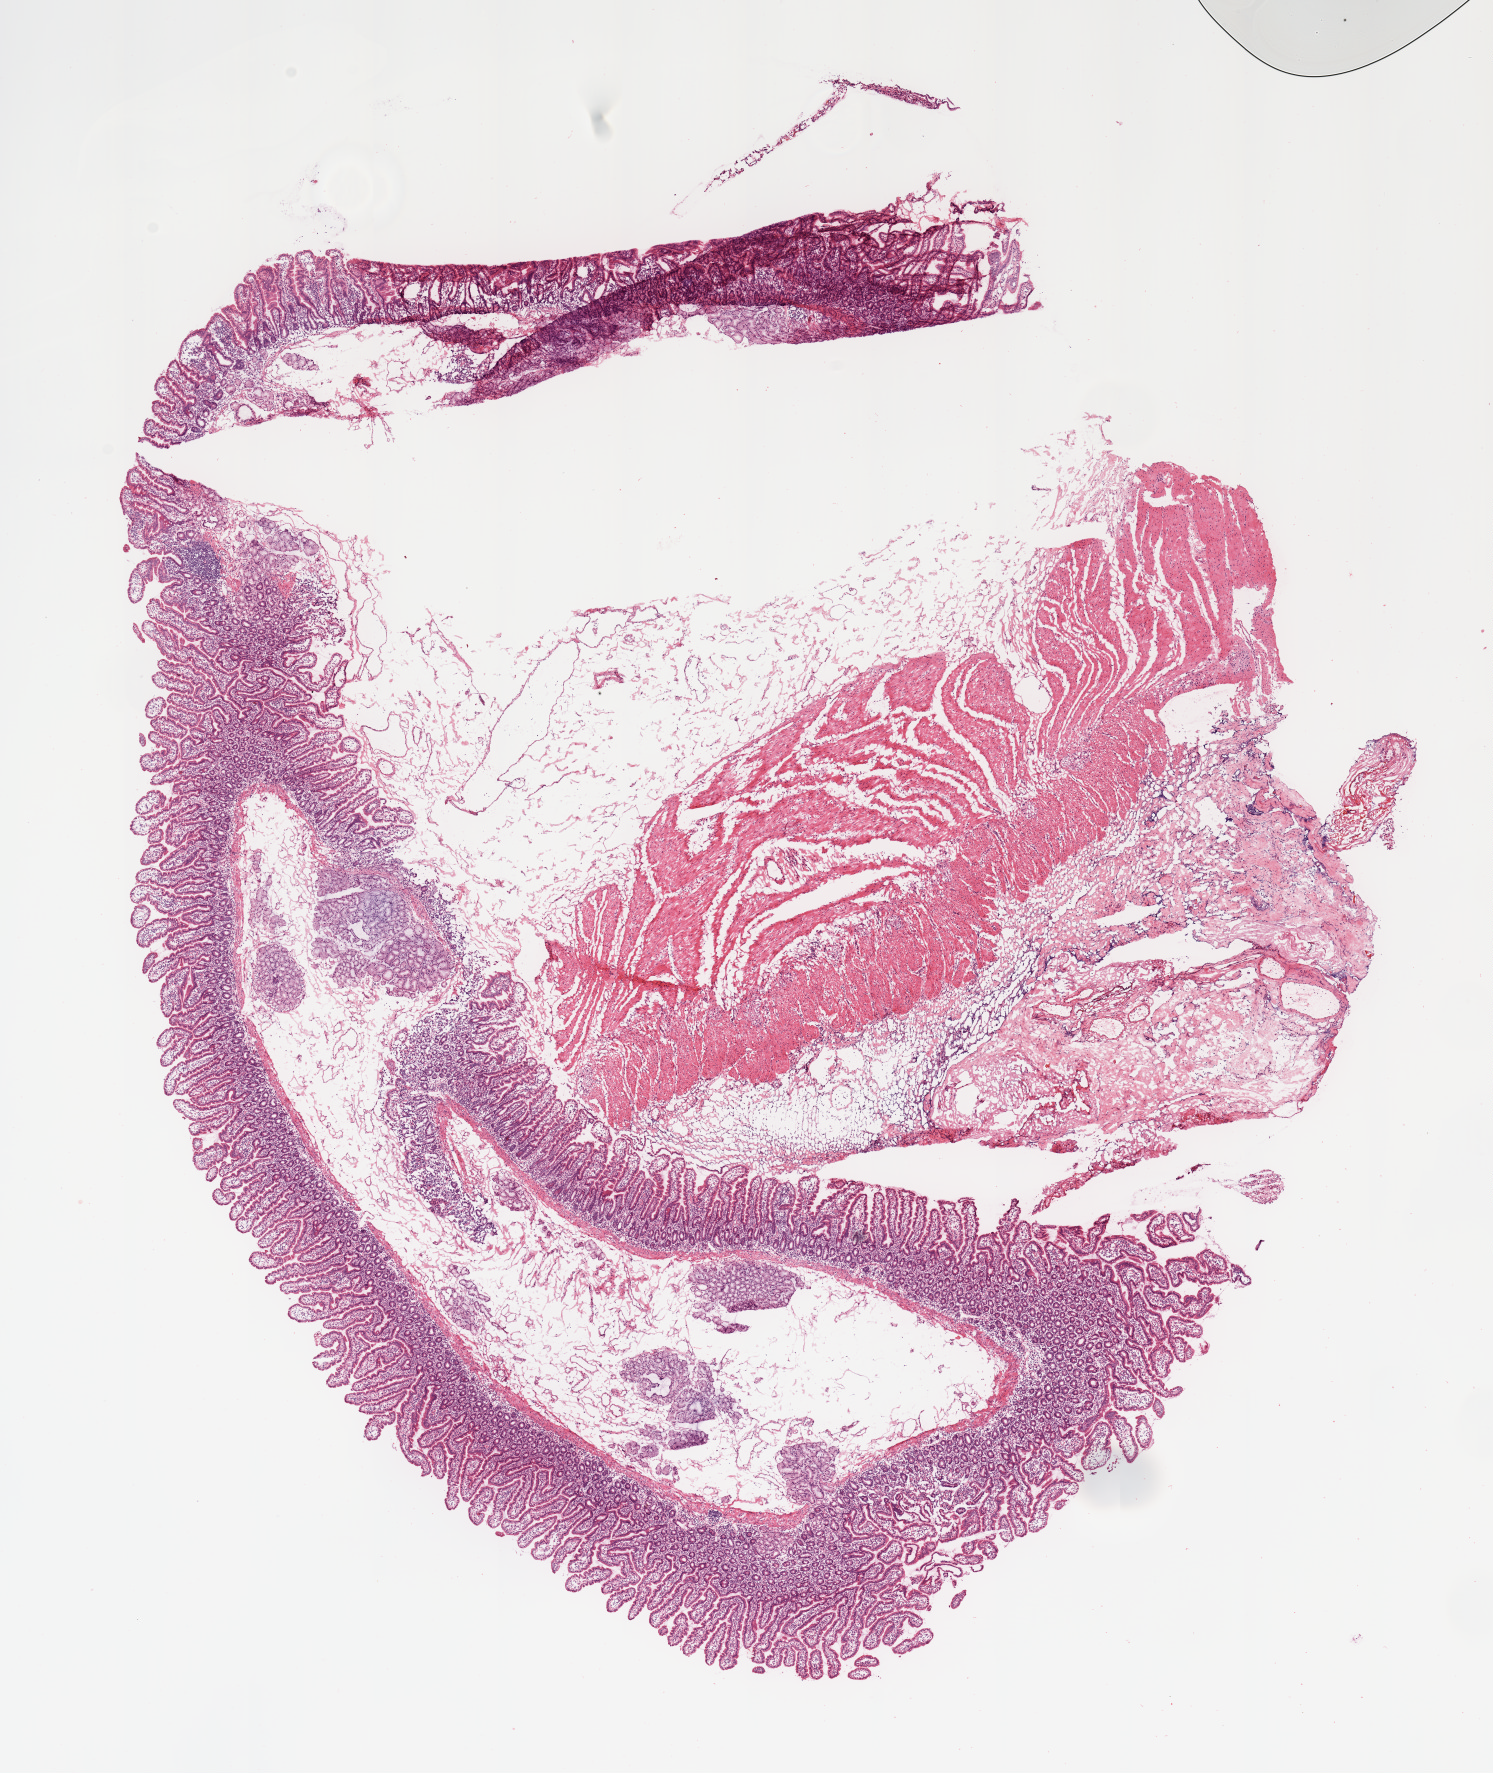
Digitized H&E tissue section (whole slide) — low-resolution overview of the scanned area, about 11.8 x 14.0 mm (slide scanned at 20x). Pancreas, normal (non-tumour) tissue. Patient: male, age 69 years.
This section: normal (non-tumour) tissue from the same patient. Patient diagnosis: Infiltrating duct carcinoma, NOS.